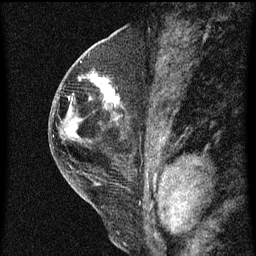
Breast MRI (dynamic contrast-enhanced), one sagittal slice. Position 29 of 60 along the scan axis. Dynamic contrast-enhanced series, image 2 of 3 at this slice position (ordered by acquisition). 1.5 T. TE 4.2 ms, TR 8 ms. 256 × 256 image matrix. Patient: female, 48 years.
Structures marked on this image (semi-automatically segmented with operator editing):
- analysis volume of interest (the breast-tissue region the enhancement analysis was run in; not a lesion): bounding box (x1, y1, x2, y2) in pixels: (89, 72, 123, 113)
- tumour enhancement mask (voxels above the 70 % enhancement threshold inside the analysis volume of interest): (93, 76, 120, 109)